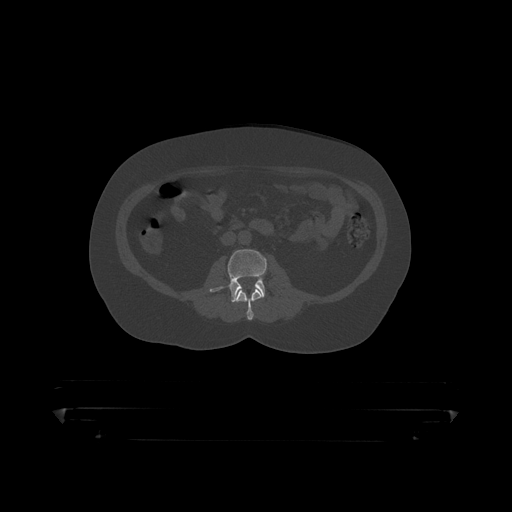
CT including the spine, one axial slice; slice 101 of 390 in the series (ordered by position); reconstruction kernel STANDARD; 120 kVp; bone window (W 1800 / L 400 HU); 1.25 mm slice thickness; 512 × 512 image matrix, field of view 650 × 650 mm. Male patient, age 60 years. Case-level facts recorded for this patient, not image findings: primary cancer: prostate.
Structures marked on this image (semi-automatic segmentation, software-assisted and operator-edited):
- L2 vertebra: box from (x=236, y=288) to (x=264, y=319) px
- L3 vertebra: (x=210, y=249)–(x=267, y=302)